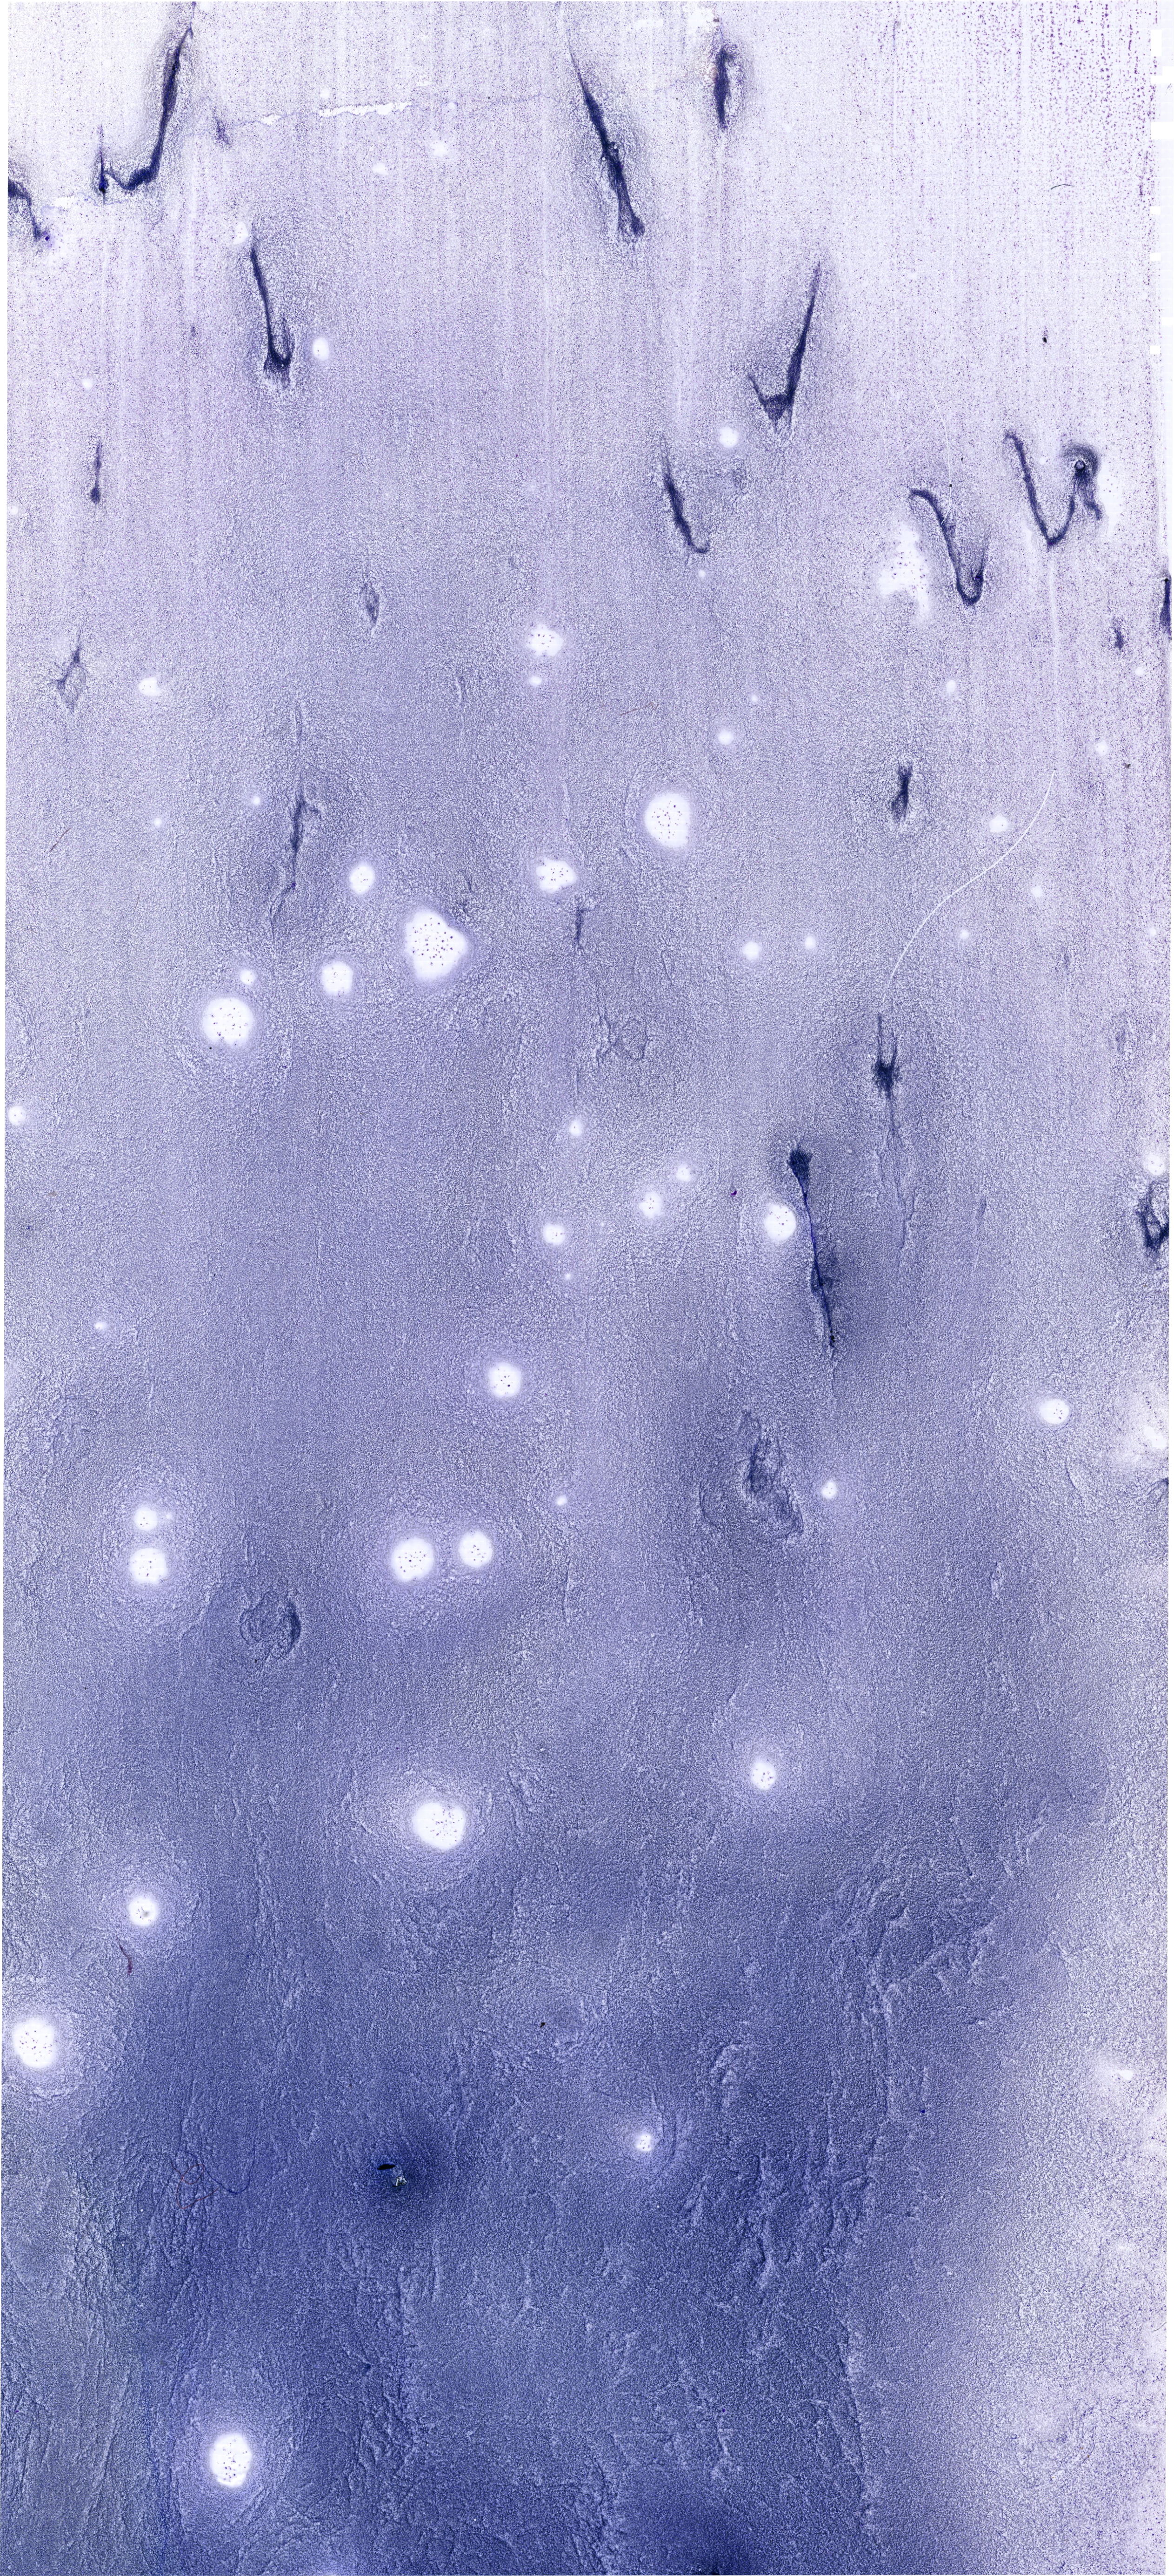
Bone marrow aspirate smear, May-Grünwald-Giemsa (MGG) stain, whole-slide image — shown as a low-resolution overview of the whole scanned area (about 19.7 x 43.2 mm). Male patient.
Diagnosis: Mixed Phenotype Acute Leukemia, B/Myeloid.